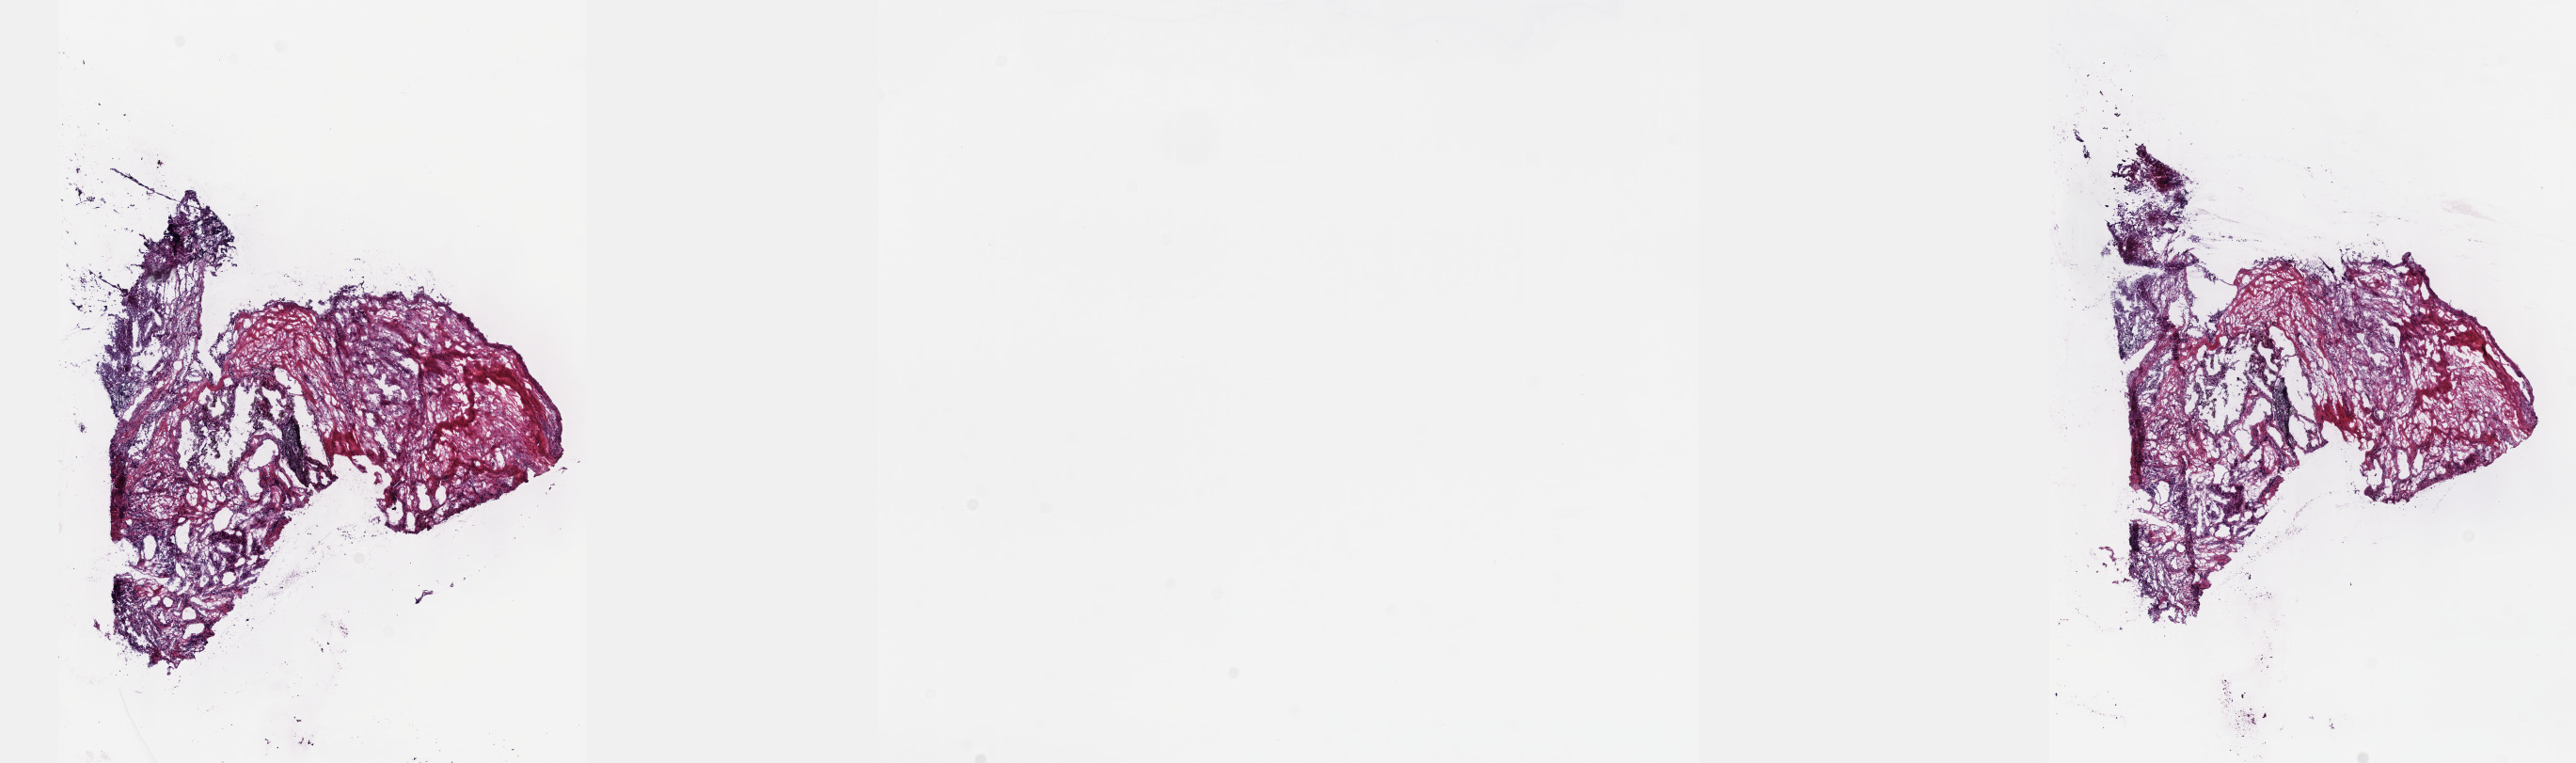
Whole-slide histology image, H&E — shown as a low-resolution overview of the whole scanned area (about 22.1 x 6.6 mm, slide scanned at 40x). Frozen section from the top of the tissue portion. Kidney, primary tumour sample. Female, age 63 years at initial diagnosis. Slide review estimates, as recorded: tumour cells 40%, tumour nuclei 75%, normal cells 0%, stromal cells 55%, necrosis 5%. Infiltration values recorded for this section: lymphocyte infiltration 6%, monocyte infiltration 4%, neutrophil infiltration 2%.
Lymph nodes positive (case pathology): 0 of 1 examined. Laterality: left. AJCC pathologic stage: II (7th edition). Pathologic diagnosis: Papillary adenocarcinoma, NOS.